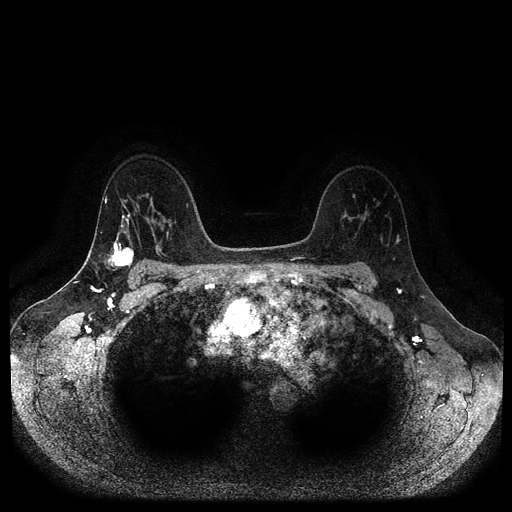
Breast MRI (dynamic contrast-enhanced, multi-phase), one axial slice; slice 72 of 116 in the series (ordered by position); dynamic contrast-enhanced series, time point 2 of 5 at this slice position (early post-contrast); 1.5 T; TE 2.6 ms, TR 5.3 ms; 2 mm slice thickness; 512 × 512 image matrix. Female patient, age 45 years.
Structures marked on this image (semi-automatic segmentation, software-assisted and operator-edited):
- breast lesion (labelled 'tumour' in the annotation; benign lesions carry a separate 'benign' label): box from (x=107, y=239) to (x=135, y=272) px